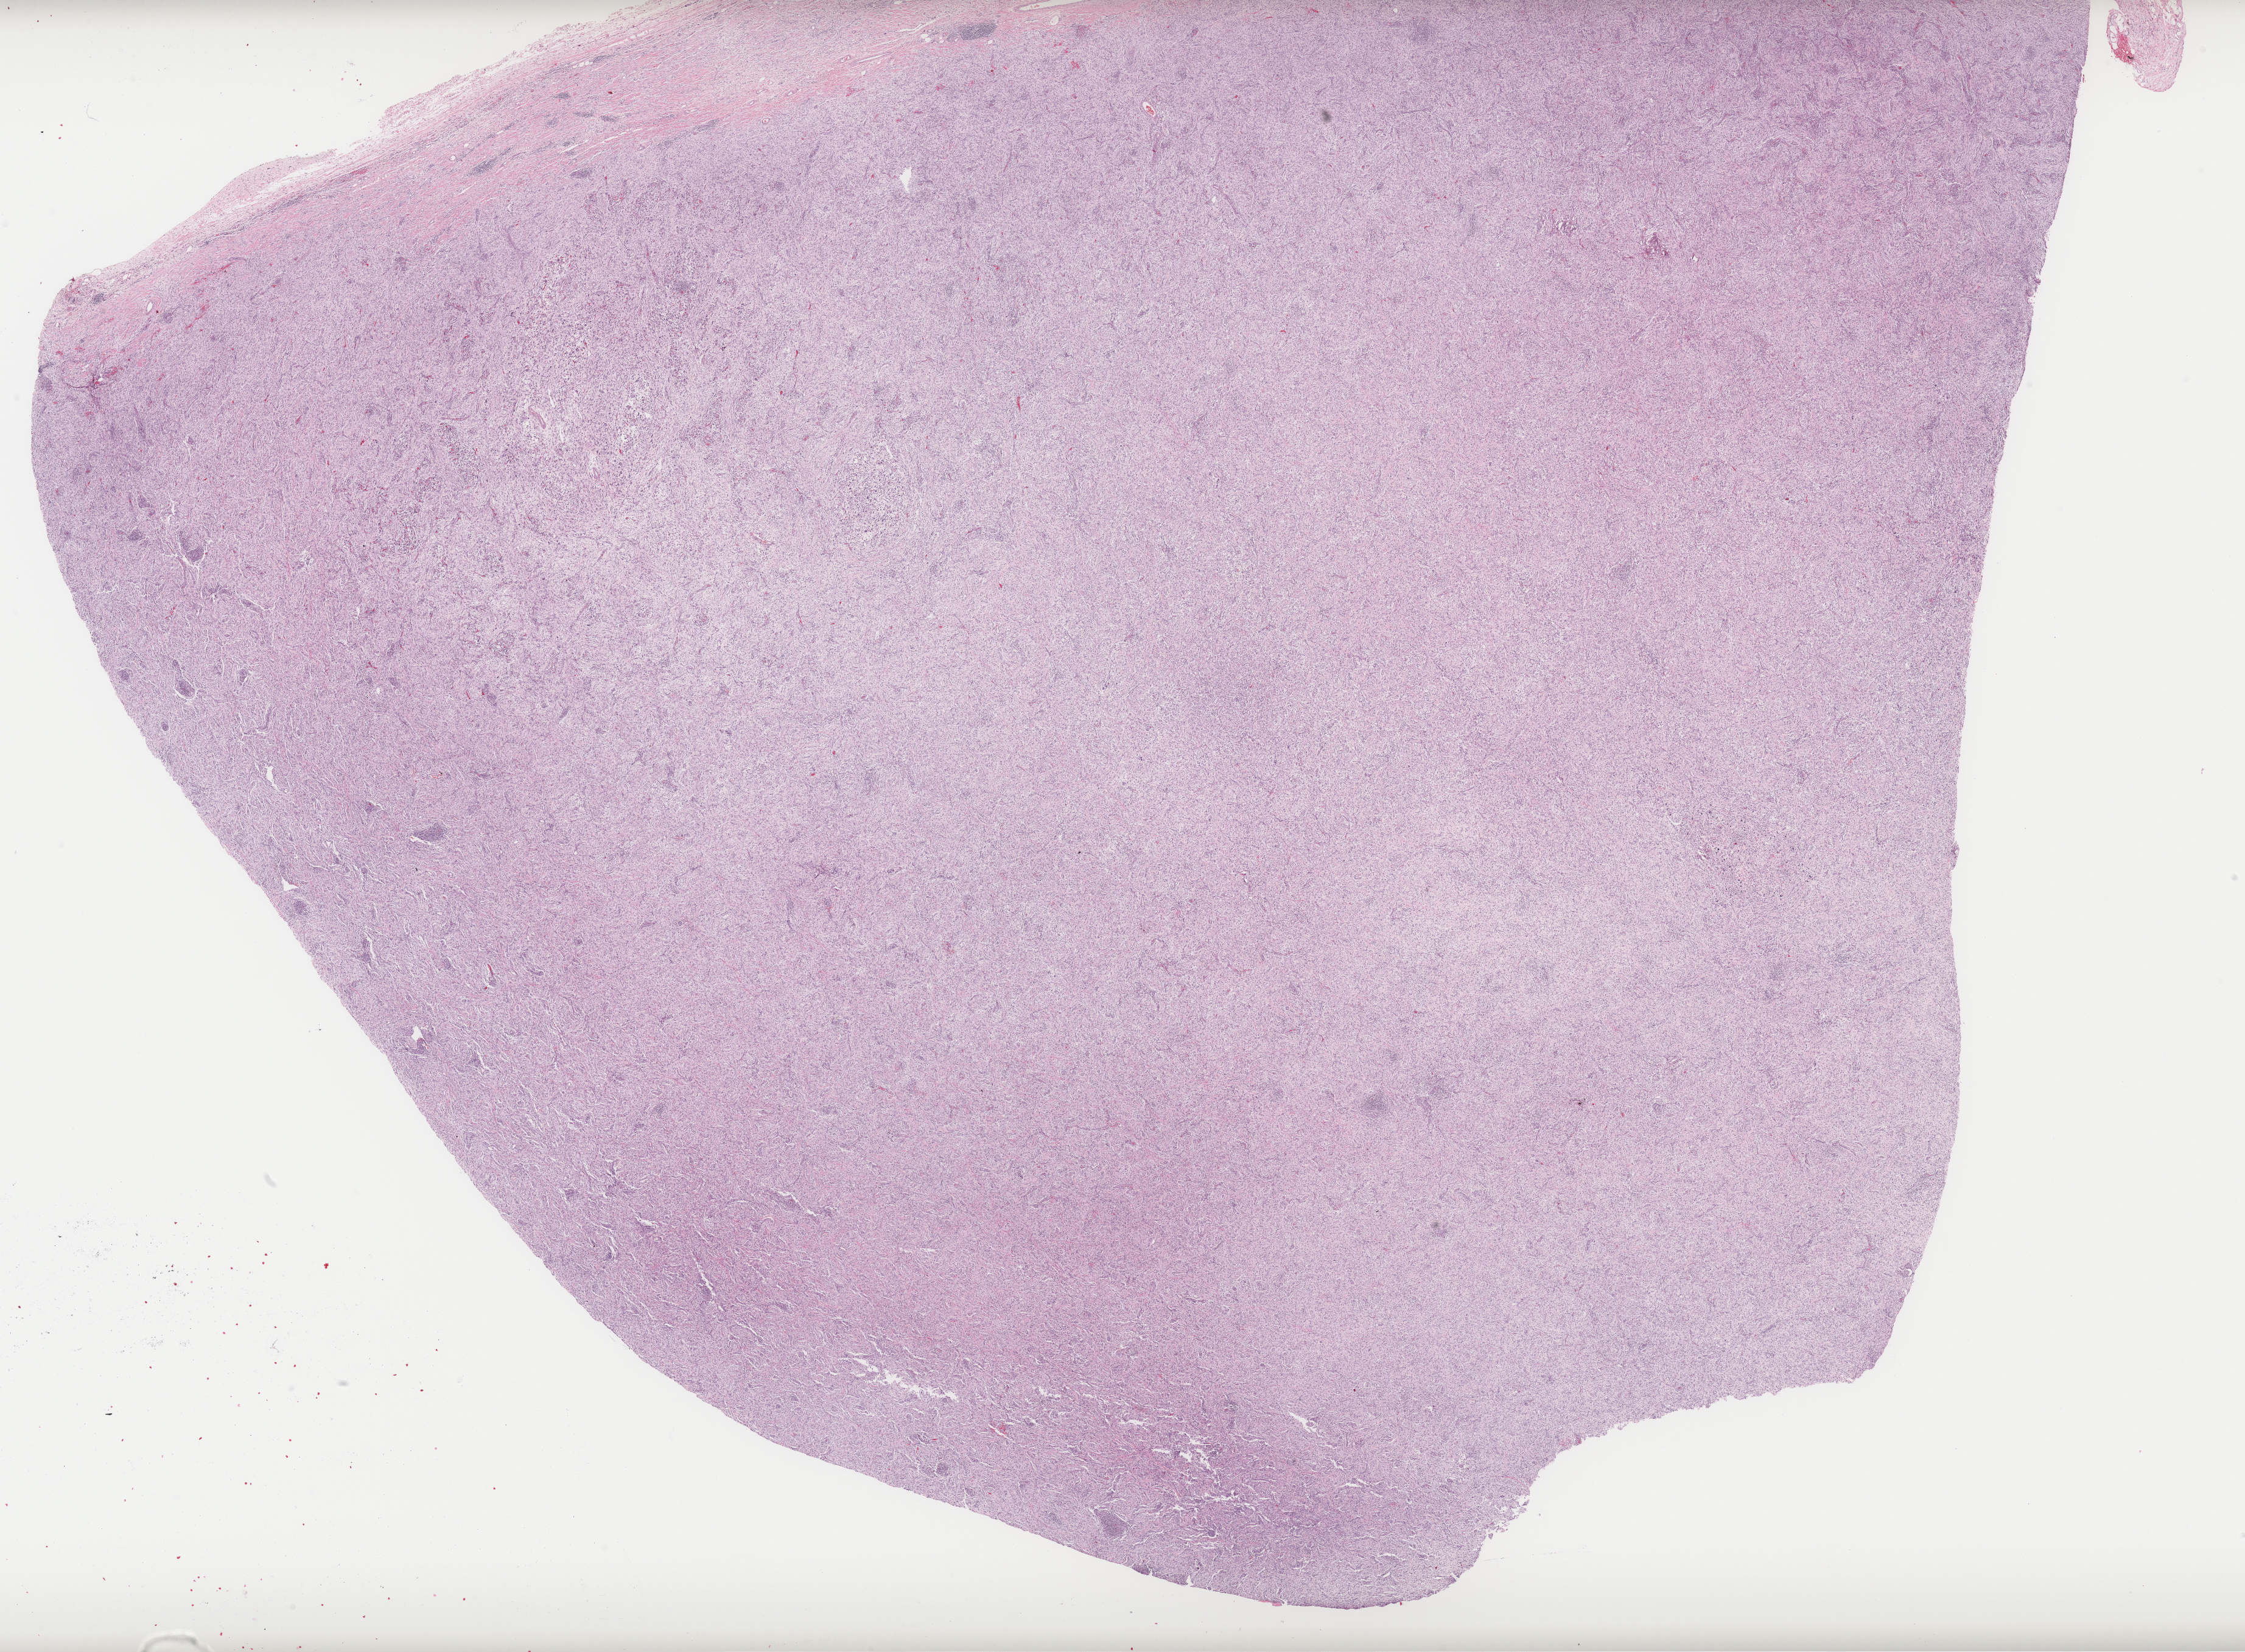
H&E-stained whole-slide image — a low-resolution overview of the entire scanned area, about 29.5 x 21.7 mm, formalin-fixed paraffin-embedded (FFPE) diagnostic section, retroperitoneum and peritoneum, primary tumour sample. Male, age 77 years at initial diagnosis.
• diagnosis: Dedifferentiated liposarcoma (retroperitoneum)